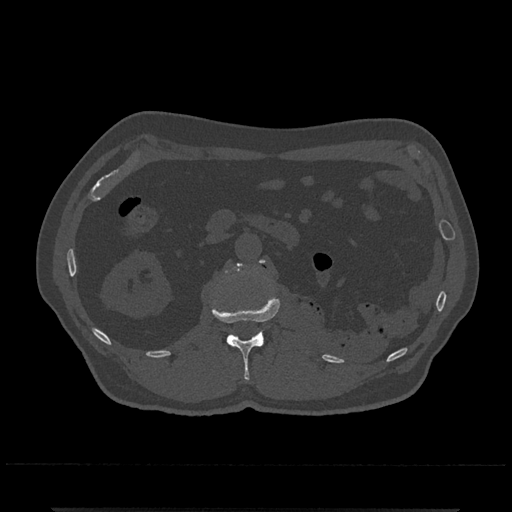
CT including the spine, one axial slice; slice 342 of 797 in the series (ordered by position); reconstruction kernel Br40s/3; 120 kVp; bone window (W 1800 / L 400 HU); 0.5 mm slice thickness; 512 × 512 image matrix, field of view 393 × 393 mm. Patient: male, 67 years. From the clinical record (not read from this slice): primary cancer: prostate.
Structures marked on this image (semi-automatic segmentation, software-assisted and operator-edited):
- L1 vertebra: box from (x=212, y=297) to (x=280, y=380) px
- L2 vertebra: (x=226, y=260)–(x=265, y=273)